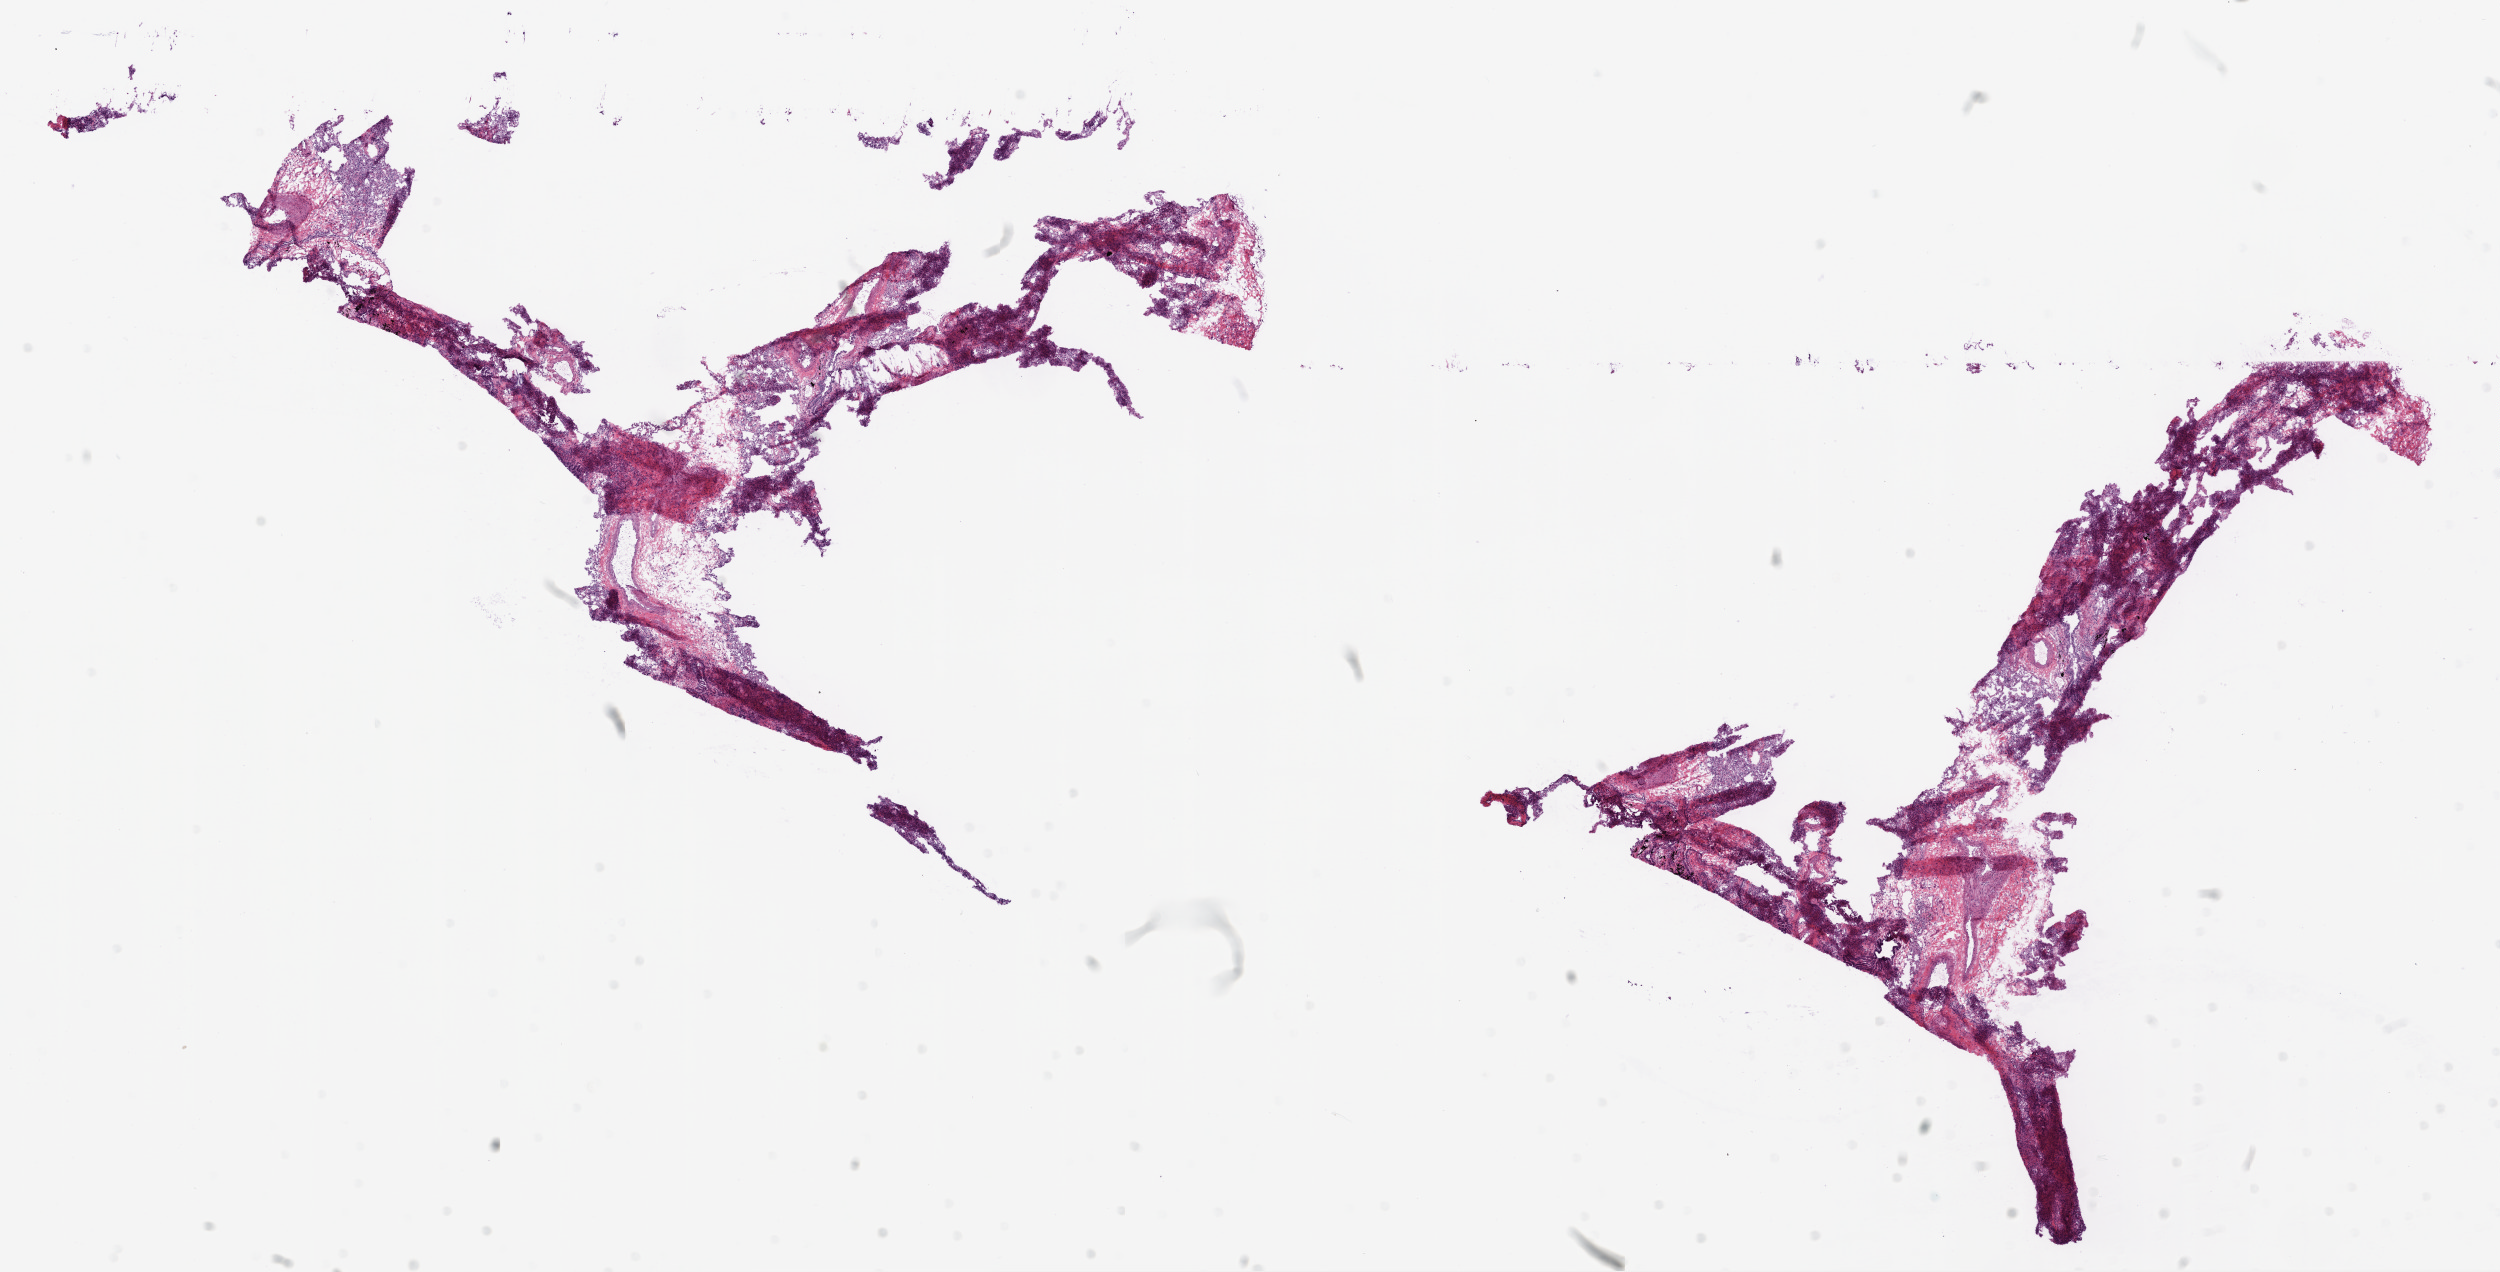
Whole-slide histology image, H&E-stained — a low-resolution overview of the entire scanned area, about 20.1 x 10.2 mm (acquisition: 20x scan); frozen section from the bottom of the tissue portion; sample: solid tissue normal (non-tumour tissue), lung. Male, age 66 years at initial diagnosis.
This section: solid tissue normal (non-tumour) sample from the same patient. Patient diagnosis: Squamous cell carcinoma, NOS (lower lobe, lung).